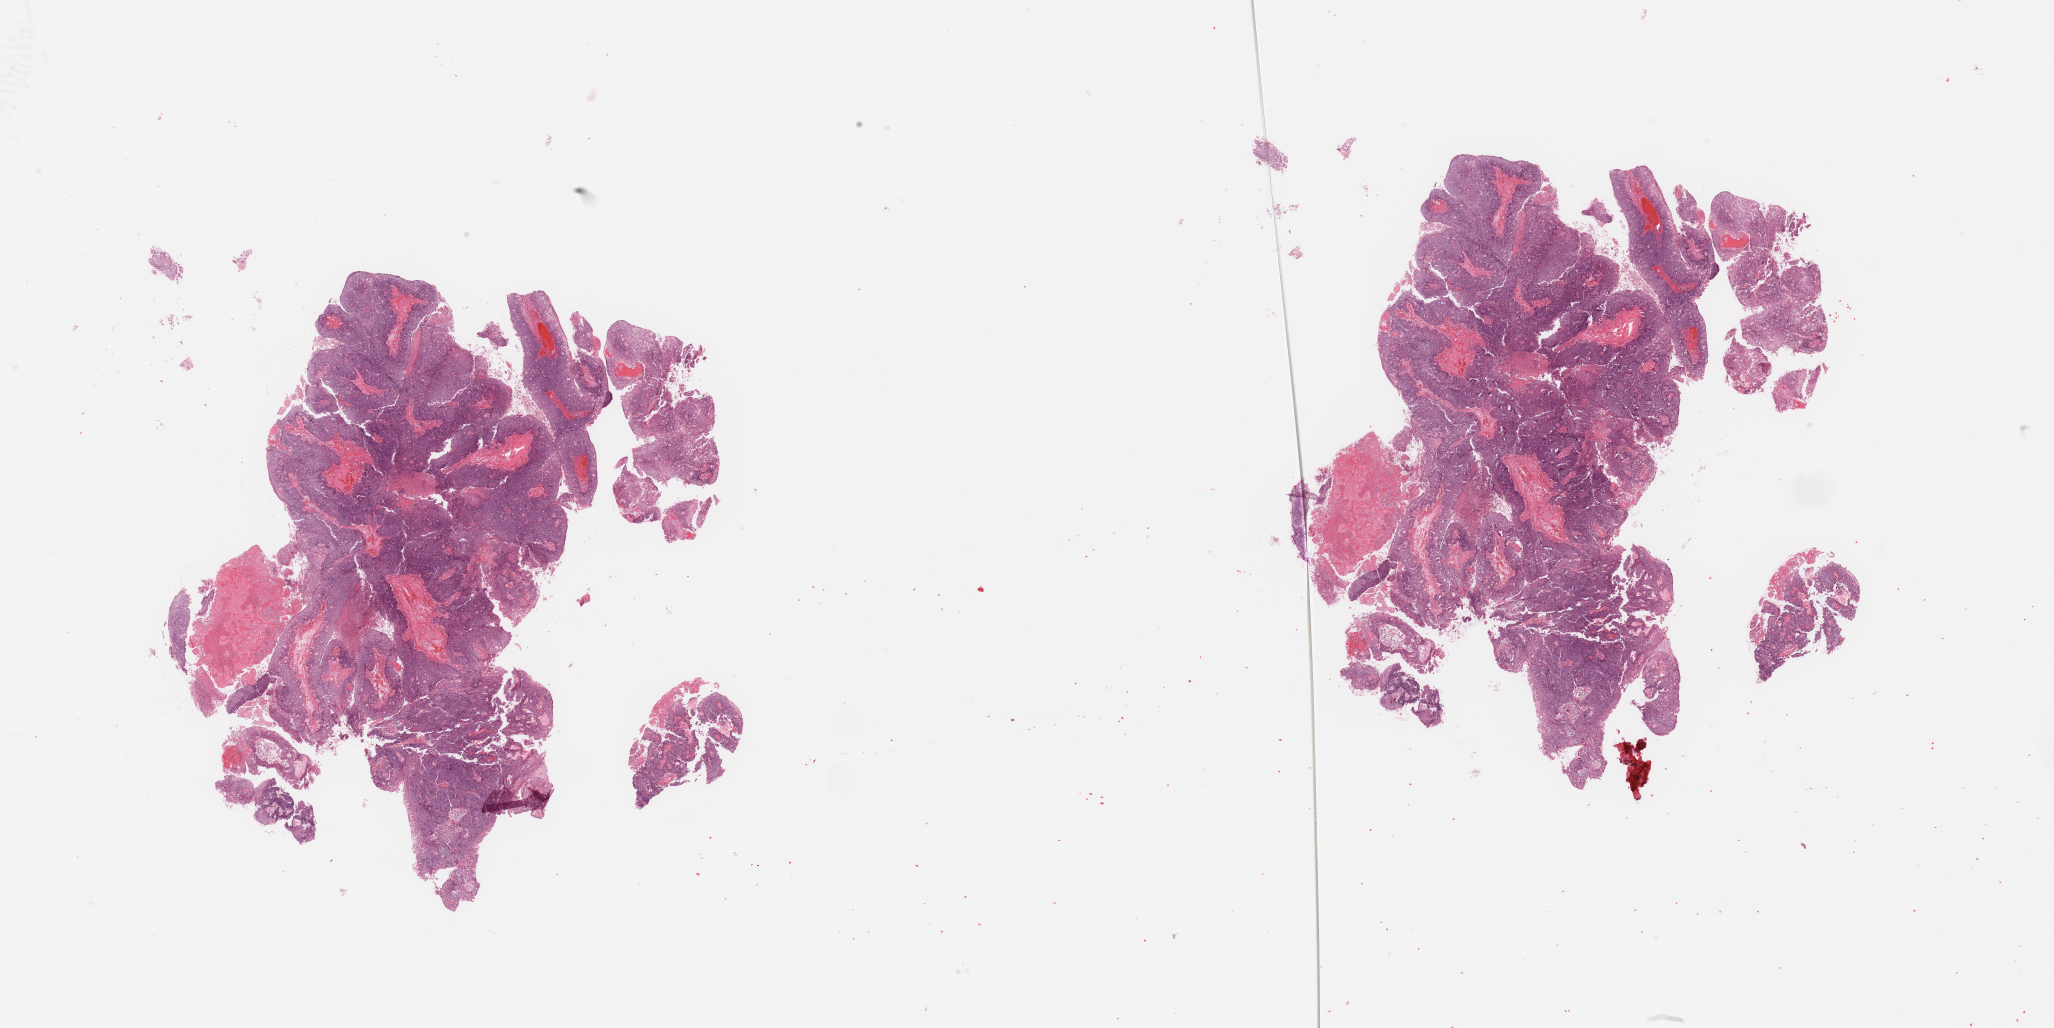
Hematoxylin and eosin (H&E) stained whole-slide image — low-resolution overview of the scanned area, about 32.5 x 16.3 mm (from a 20x scan), tumour tissue sample, sampled site: uterus. Female, 53 y/o. Histologic grade: G2 (moderately differentiated). Pathologist review of this section (percent, as recorded): tumour nuclei 90%, necrosis 10%.
• histologic diagnosis: Endometrioid adenocarcinoma, NOS
• AJCC pathologic stage: II